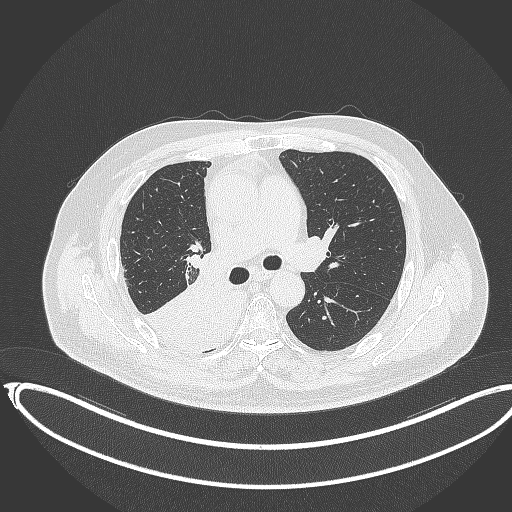
Chest CT, one axial slice. Position 218 of 403 along the scan axis. 120 kVp. Lung window (W 1500 / L -600 HU). 512 × 512 image matrix. Patient: male, 68 years. Case-level facts recorded for this patient, not image findings: clinical TNM (as recorded): T2a N0 M0.
Structures marked on this image (bounding box drawn by a radiologist):
- lung tumour (recorded histology: adenocarcinoma): box from (x=148, y=270) to (x=246, y=349) px